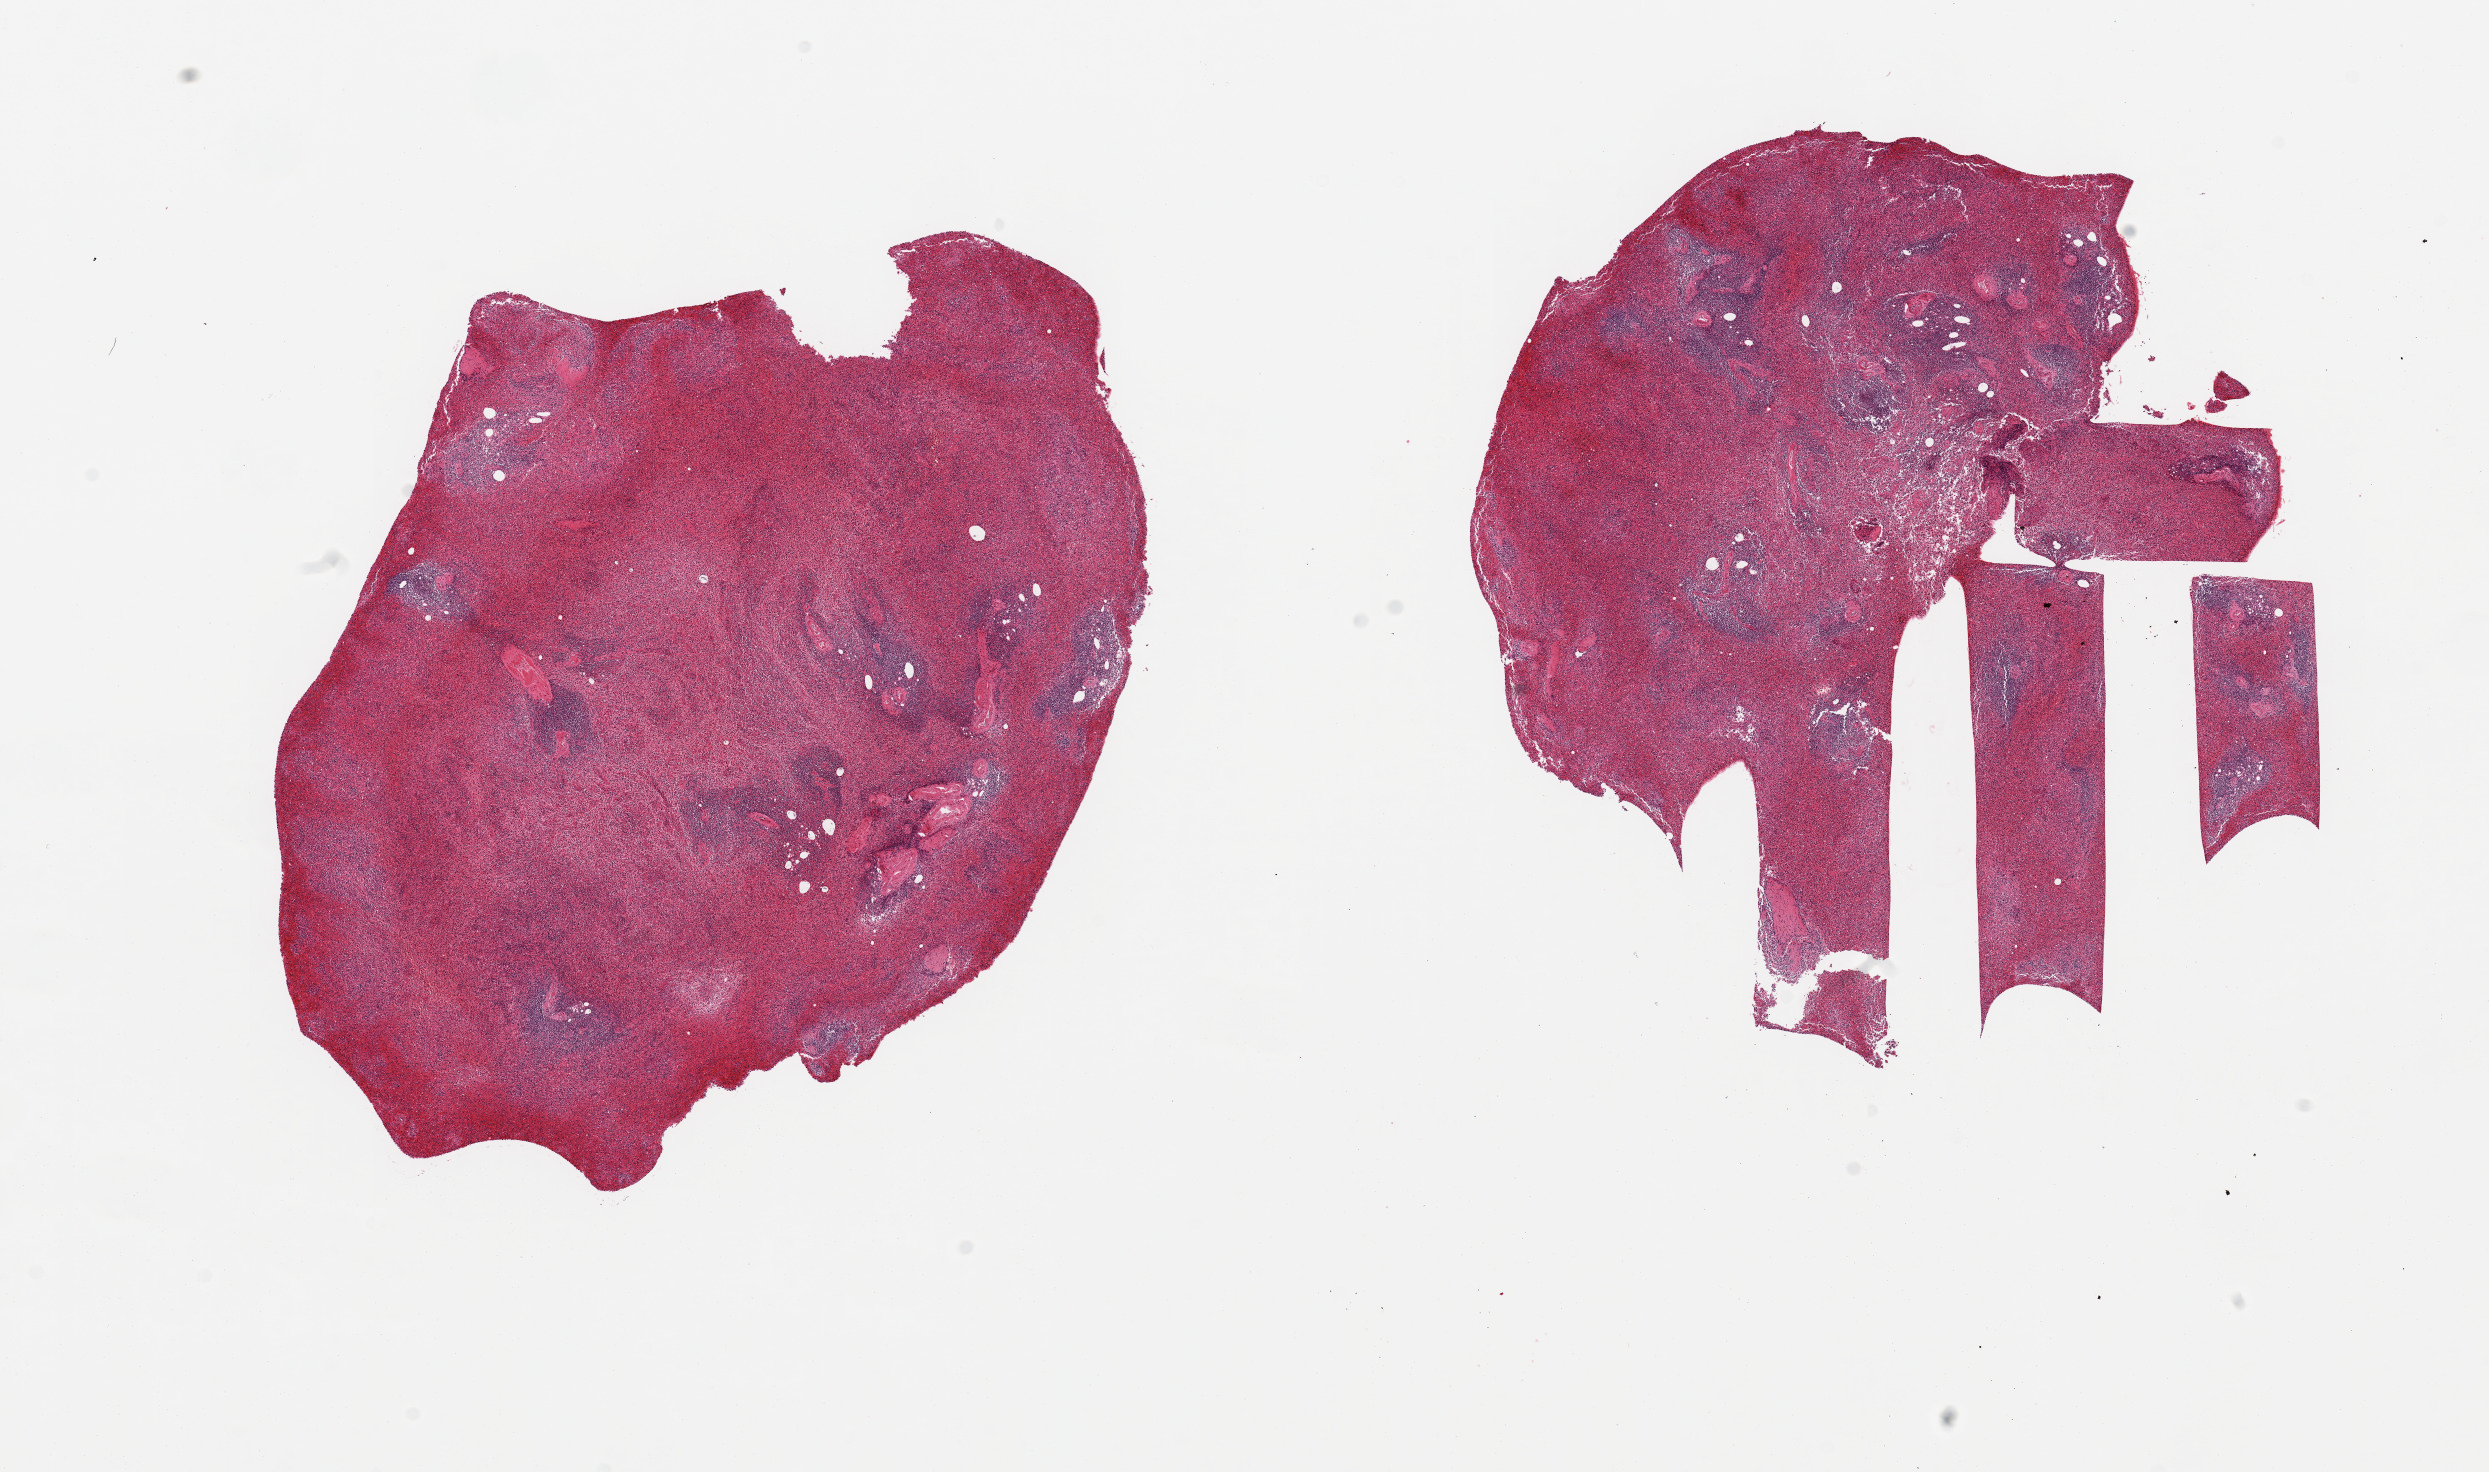
Whole-slide image, H&E stain, shown as a low-resolution overview of the whole scanned area (about 19.7 x 11.6 mm). PAXgene-fixed paraffin-embedded (PFPE) section. Section of spleen (target tissue). Donor tissue sample. Male donor.
• review note (as recorded): 2 pieces, moderate congestion